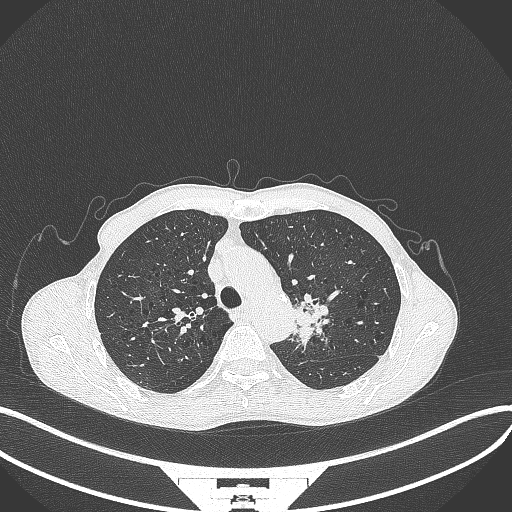
Chest CT, one axial slice; position 308 of 386 along the scan axis; 120 kVp; lung window (W 1500 / L -600 HU); 1 mm slice thickness; 512 × 512 image matrix. Patient: male, 65 years. Case-level facts recorded for this patient, not image findings: clinical TNM (as recorded): T2b N0 M0; histopathological grade: G2.
Outlined on this slice (rectangle marked by the reading radiologist):
- lung tumour (recorded histology: adenocarcinoma): bounding box [x1, y1, x2, y2] px = [291, 286, 332, 354]